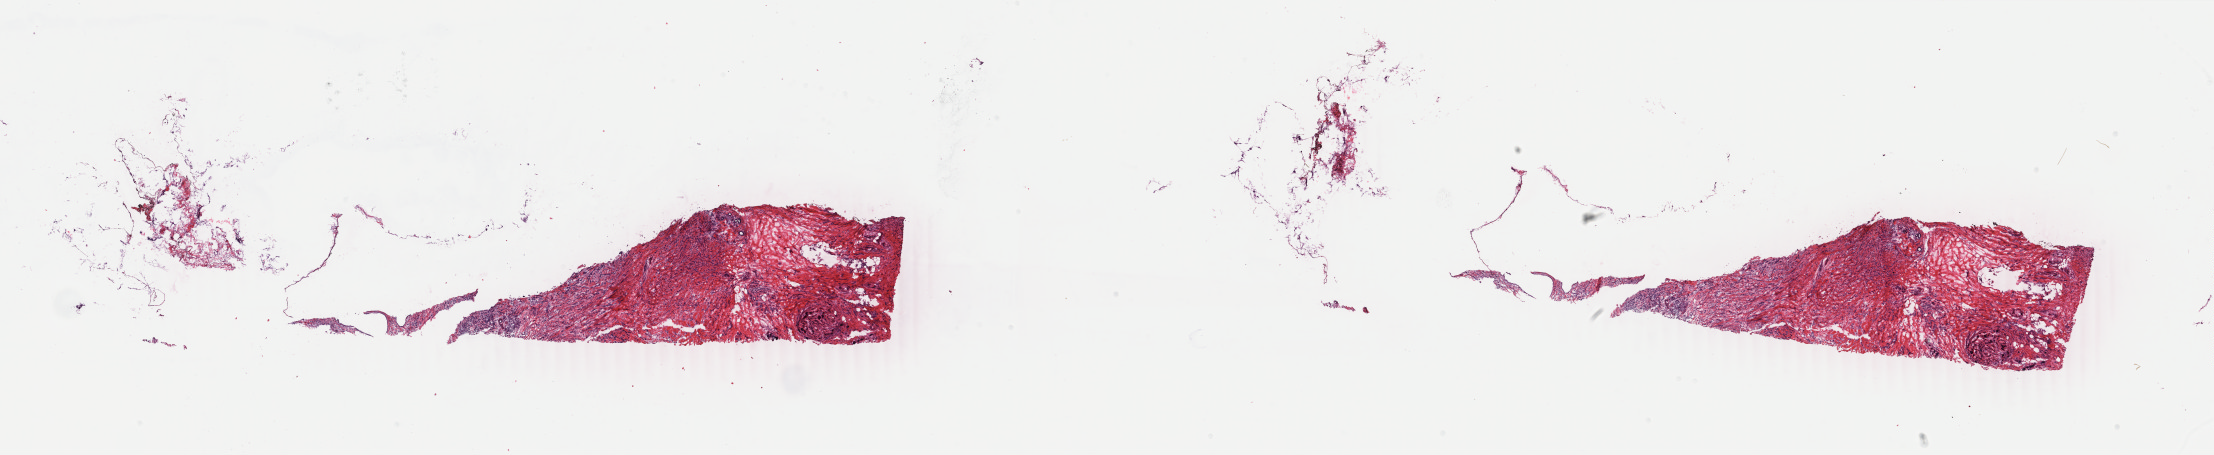
Hematoxylin and eosin (H&E) stained whole-slide image, low-resolution overview of the scanned area, about 35.2 x 7.2 mm (slide scanned at 40x), frozen section from the bottom of the tissue portion, sample: primary tumour, breast. Female, age 62 years at initial diagnosis. Pathologist review of this section (percent, as recorded): tumour cells 70%, tumour nuclei 80%, normal cells 5%, stromal cells 25%, necrosis 0%. Infiltration values recorded for this section: lymphocyte infiltration 0%, monocyte infiltration 0%, neutrophil infiltration 0%.
* AJCC pathologic stage: IIA
* histologic diagnosis: Lobular carcinoma, NOS